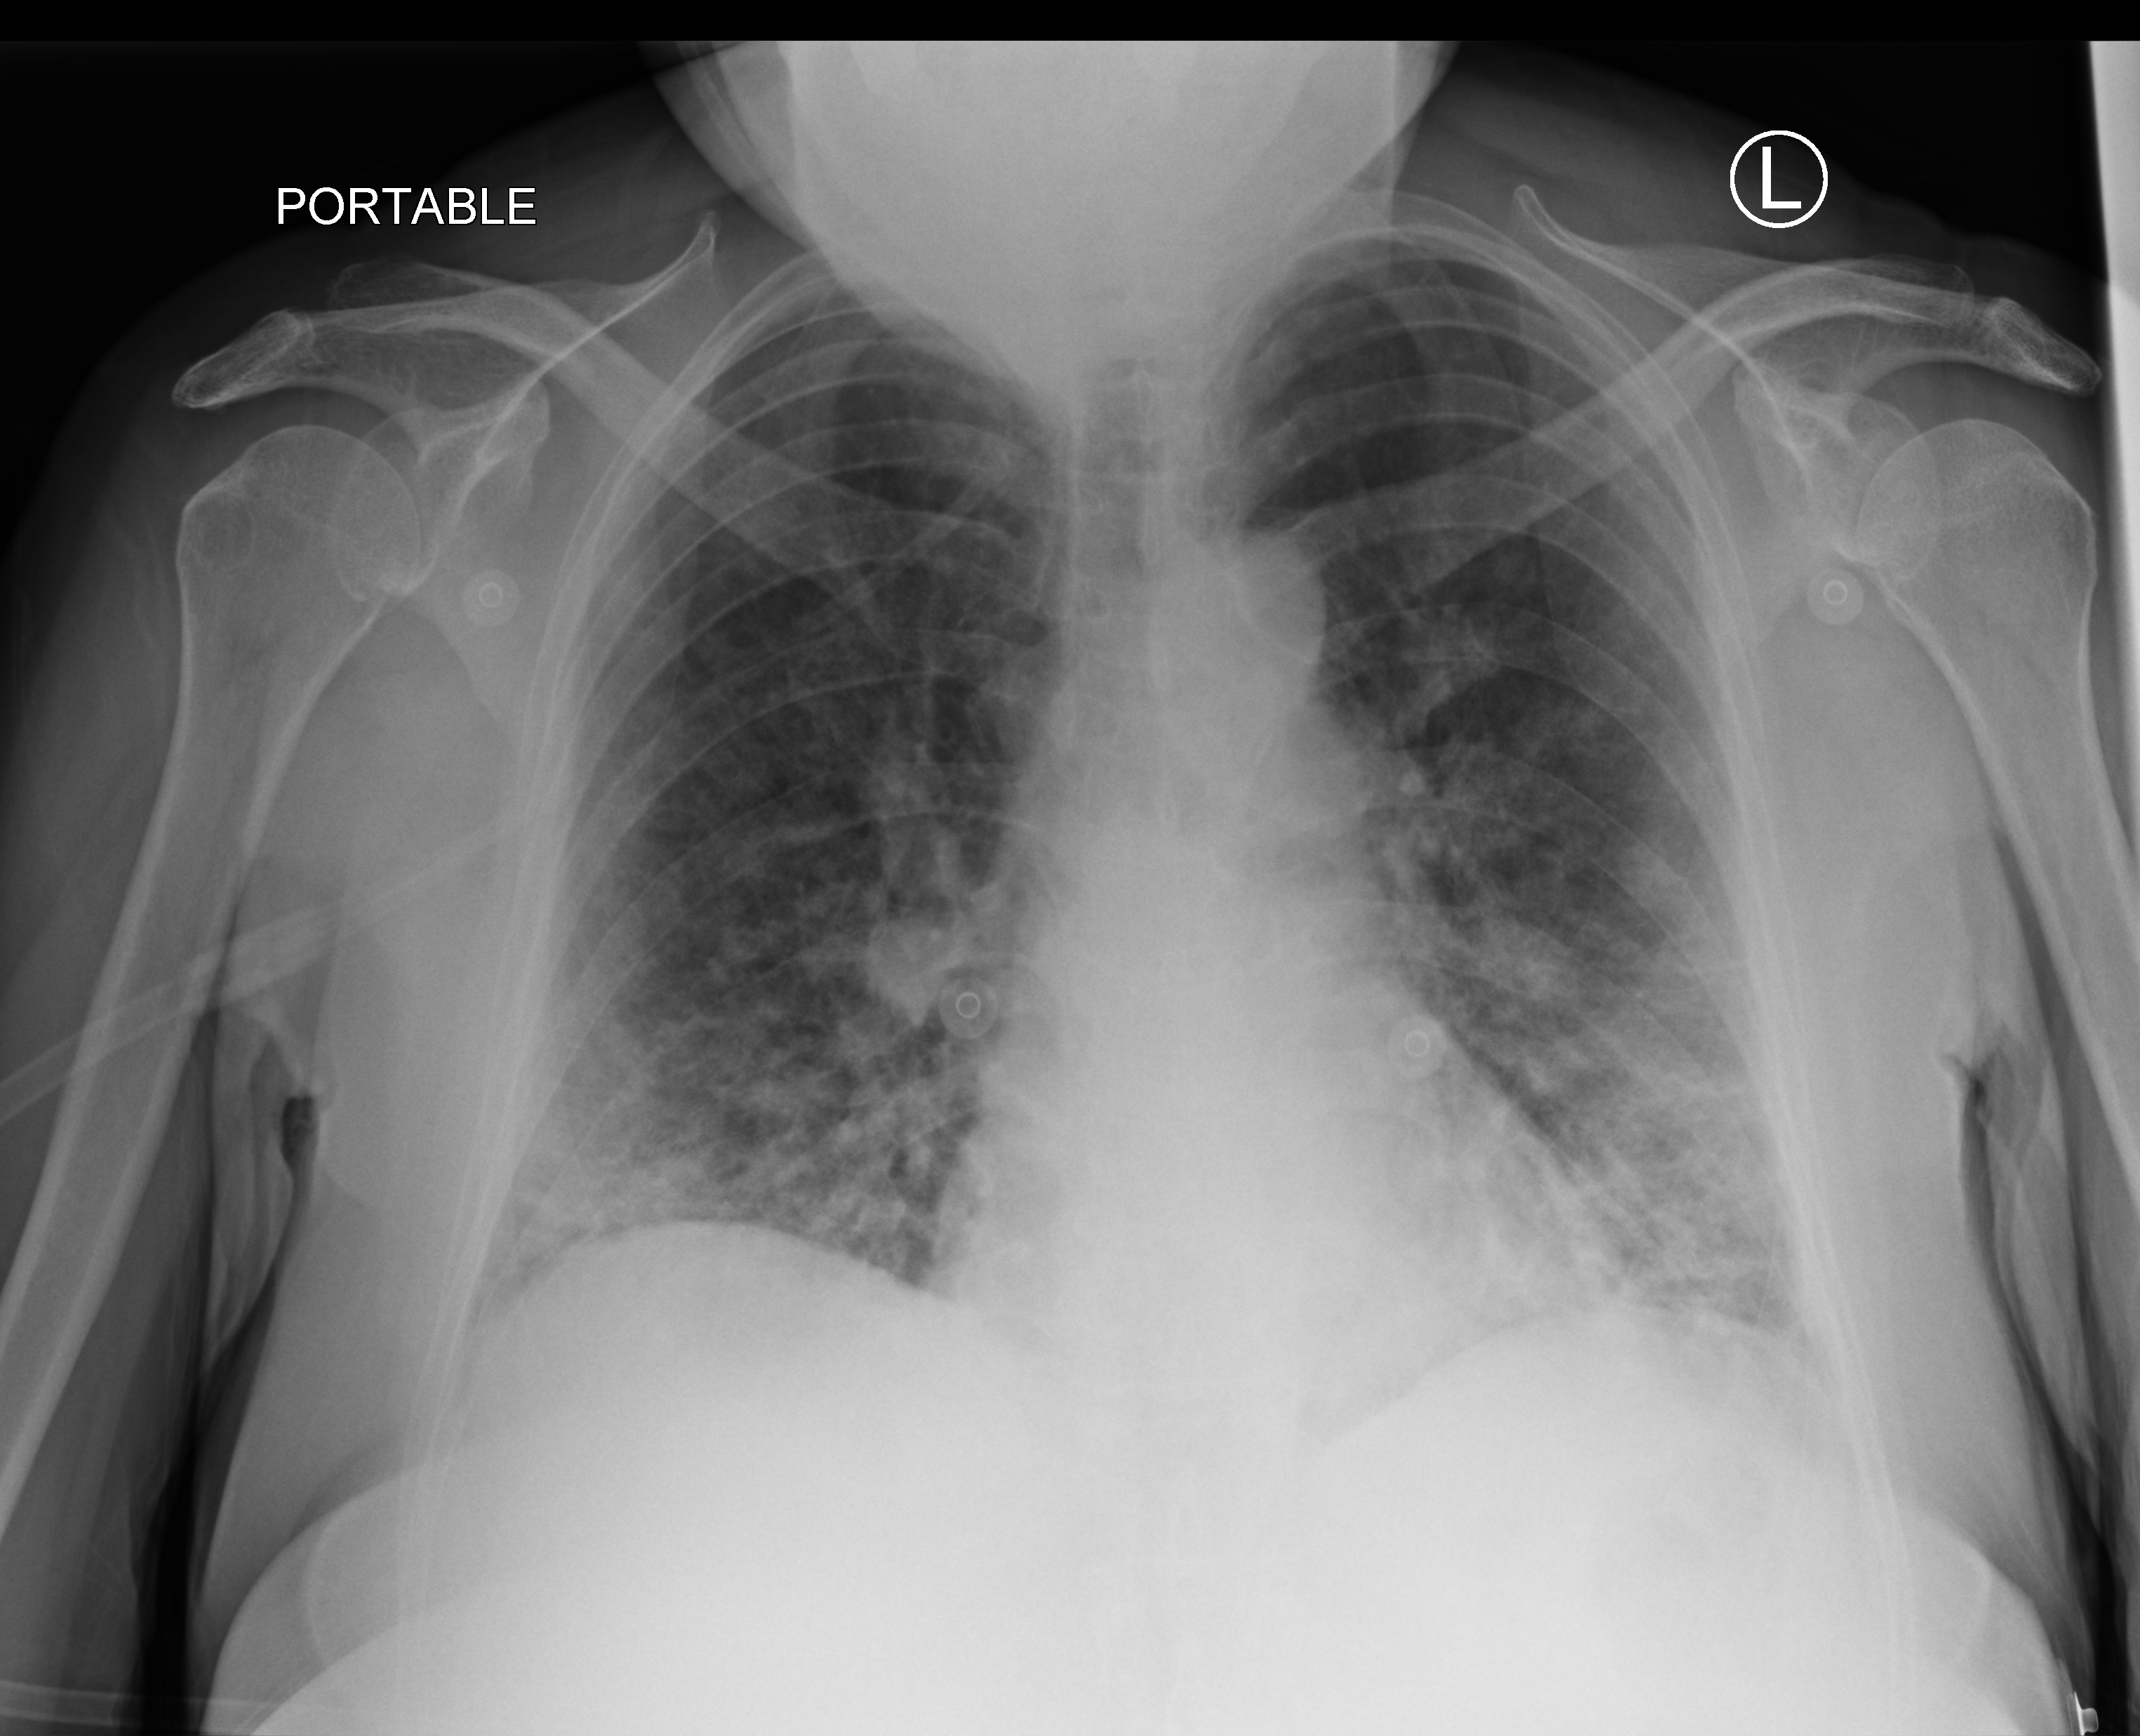
Portable chest radiograph; anteroposterior (AP) projection. Female patient hospitalised with COVID-19, age 60–74 years.
Admission-level facts for this patient (not findings on this image; timing relative to this image not recorded): admitted to intensive care during this hospital stay: no; chronic kidney disease (admission record): no.